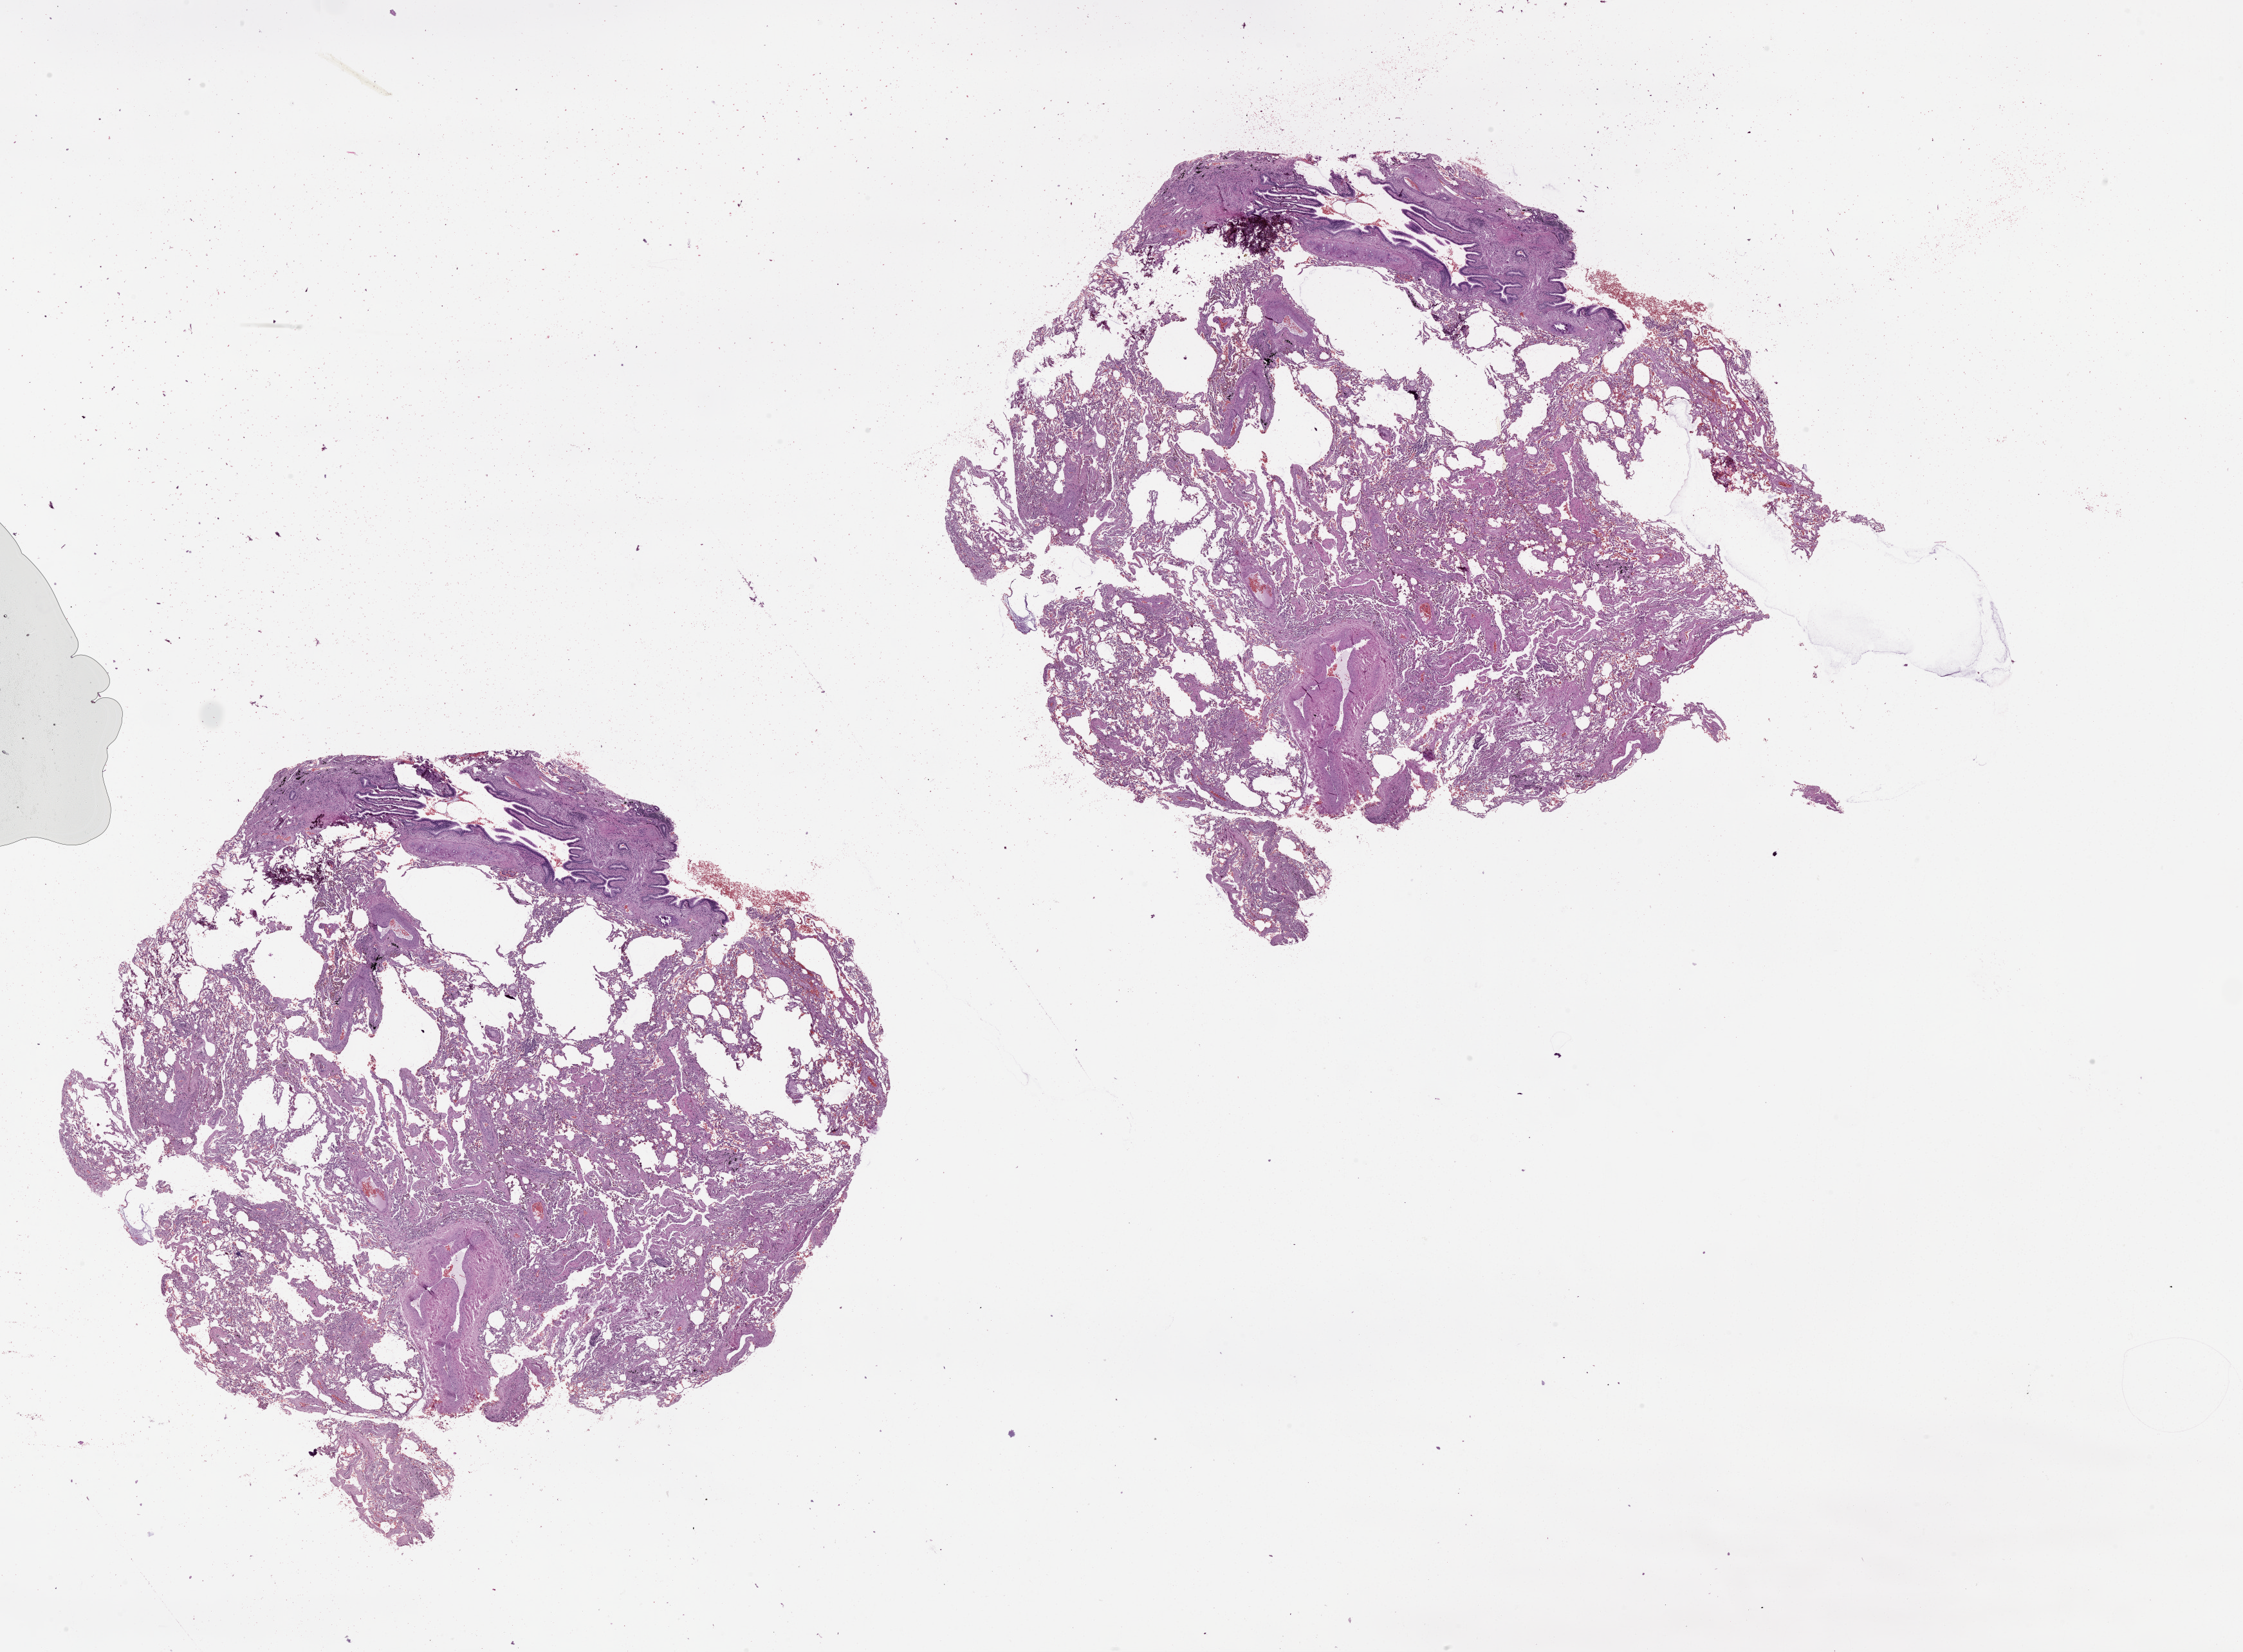
Digitized Hematoxylin and eosin (H&E) stained tissue section (whole slide) — a low-resolution overview of the entire scanned area, about 28.1 x 20.7 mm (acquisition: 20x scan). Normal (non-tumour) tissue sample, lung. Patient: male, age 67 years.
This section: normal (non-tumour) tissue from the same patient. Patient diagnosis (cohort enrolment): squamous cell carcinoma (lung).